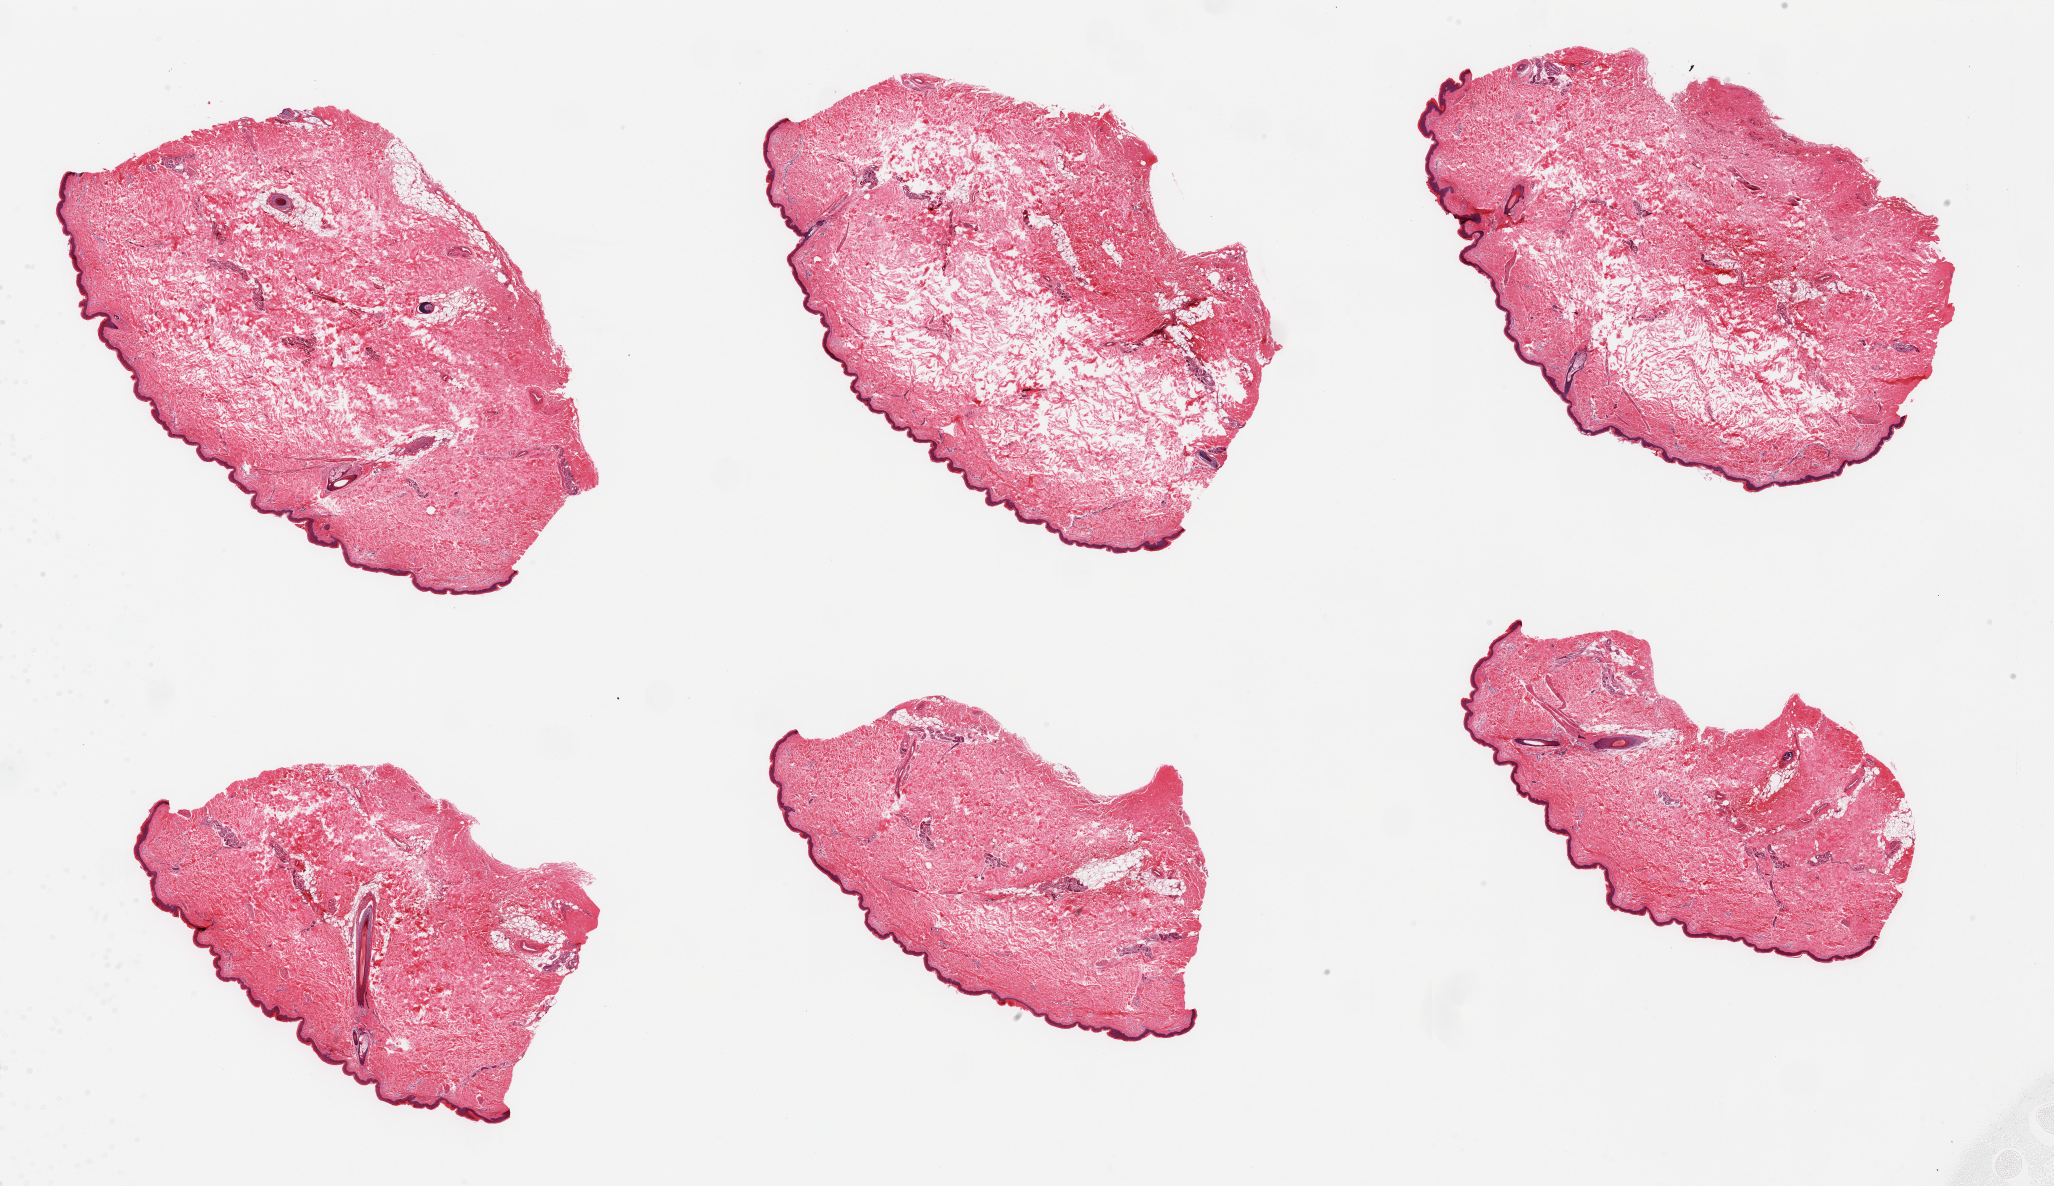
Digitized H&E-stained section, whole scanned area (about 32.5 x 18.8 mm) shown as a low-resolution overview. PAXgene-fixed, paraffin-embedded tissue. Section of skin of lower leg (target tissue). Donor tissue sample. Donor: male.
* review note (as recorded): 6 pieces, no dermal fat, squamous epithelium is ~50 microns